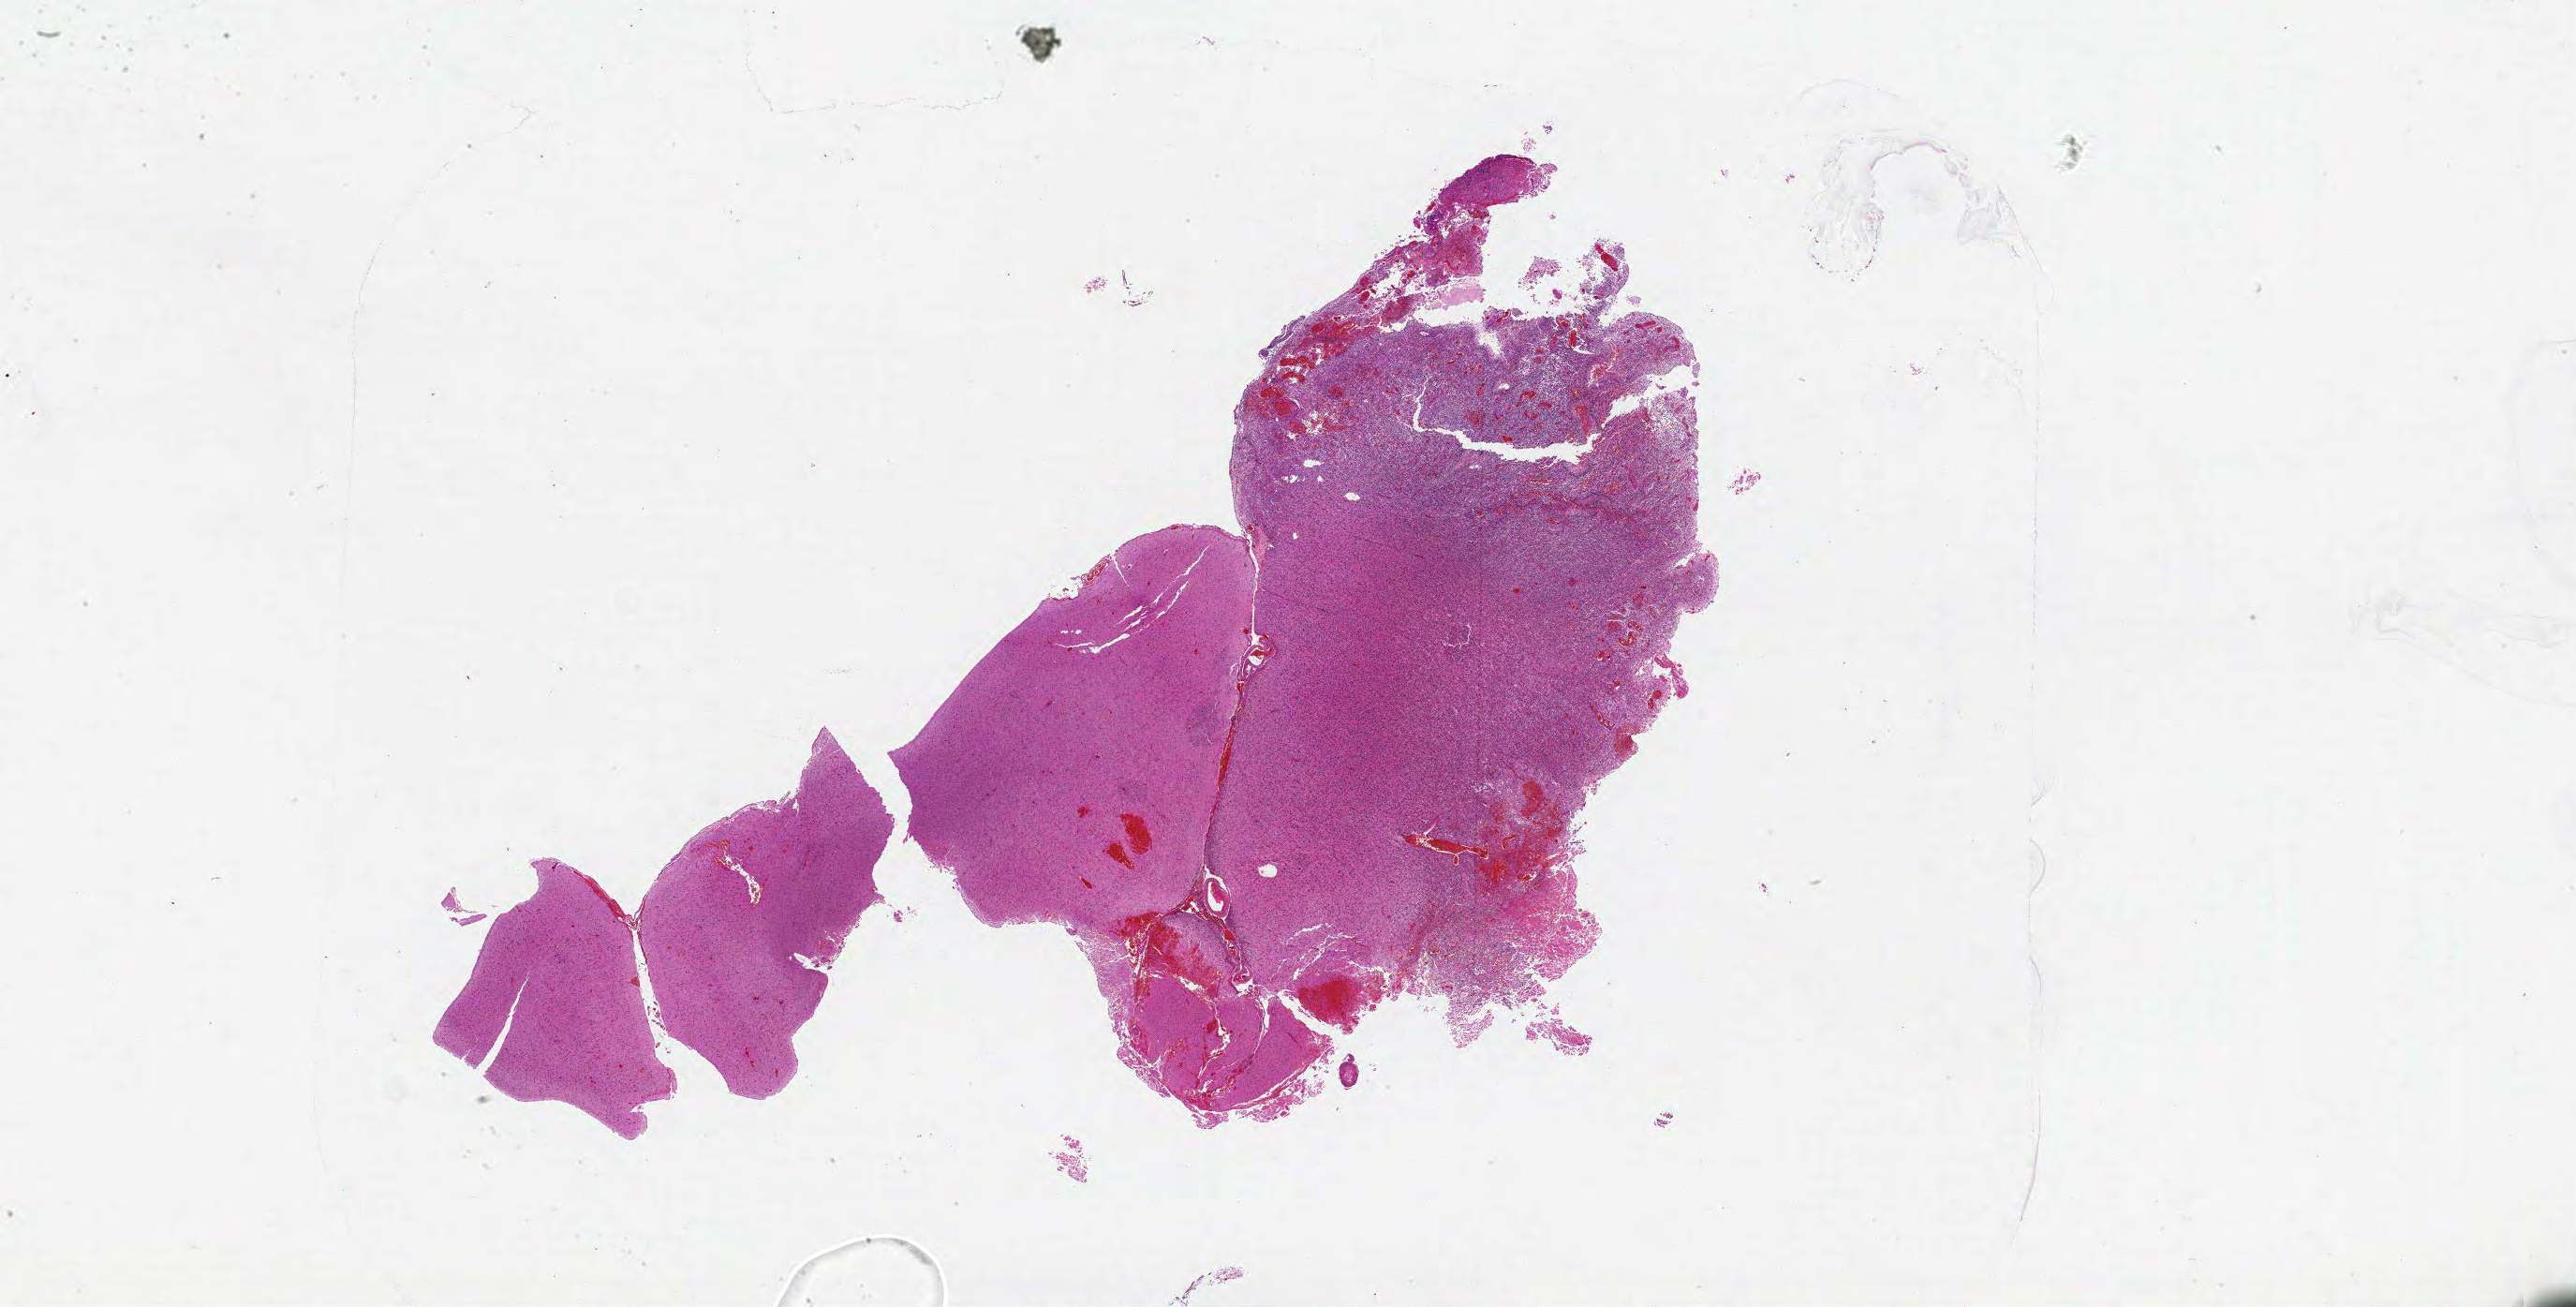
Whole-slide histology image, H&E-stained — low-resolution overview of the scanned area, about 44.0 x 22.3 mm; formalin-fixed paraffin-embedded (FFPE) diagnostic section; brain, primary tumour sample. Male, age 55 years at initial diagnosis.
Diagnosis: Glioblastoma.